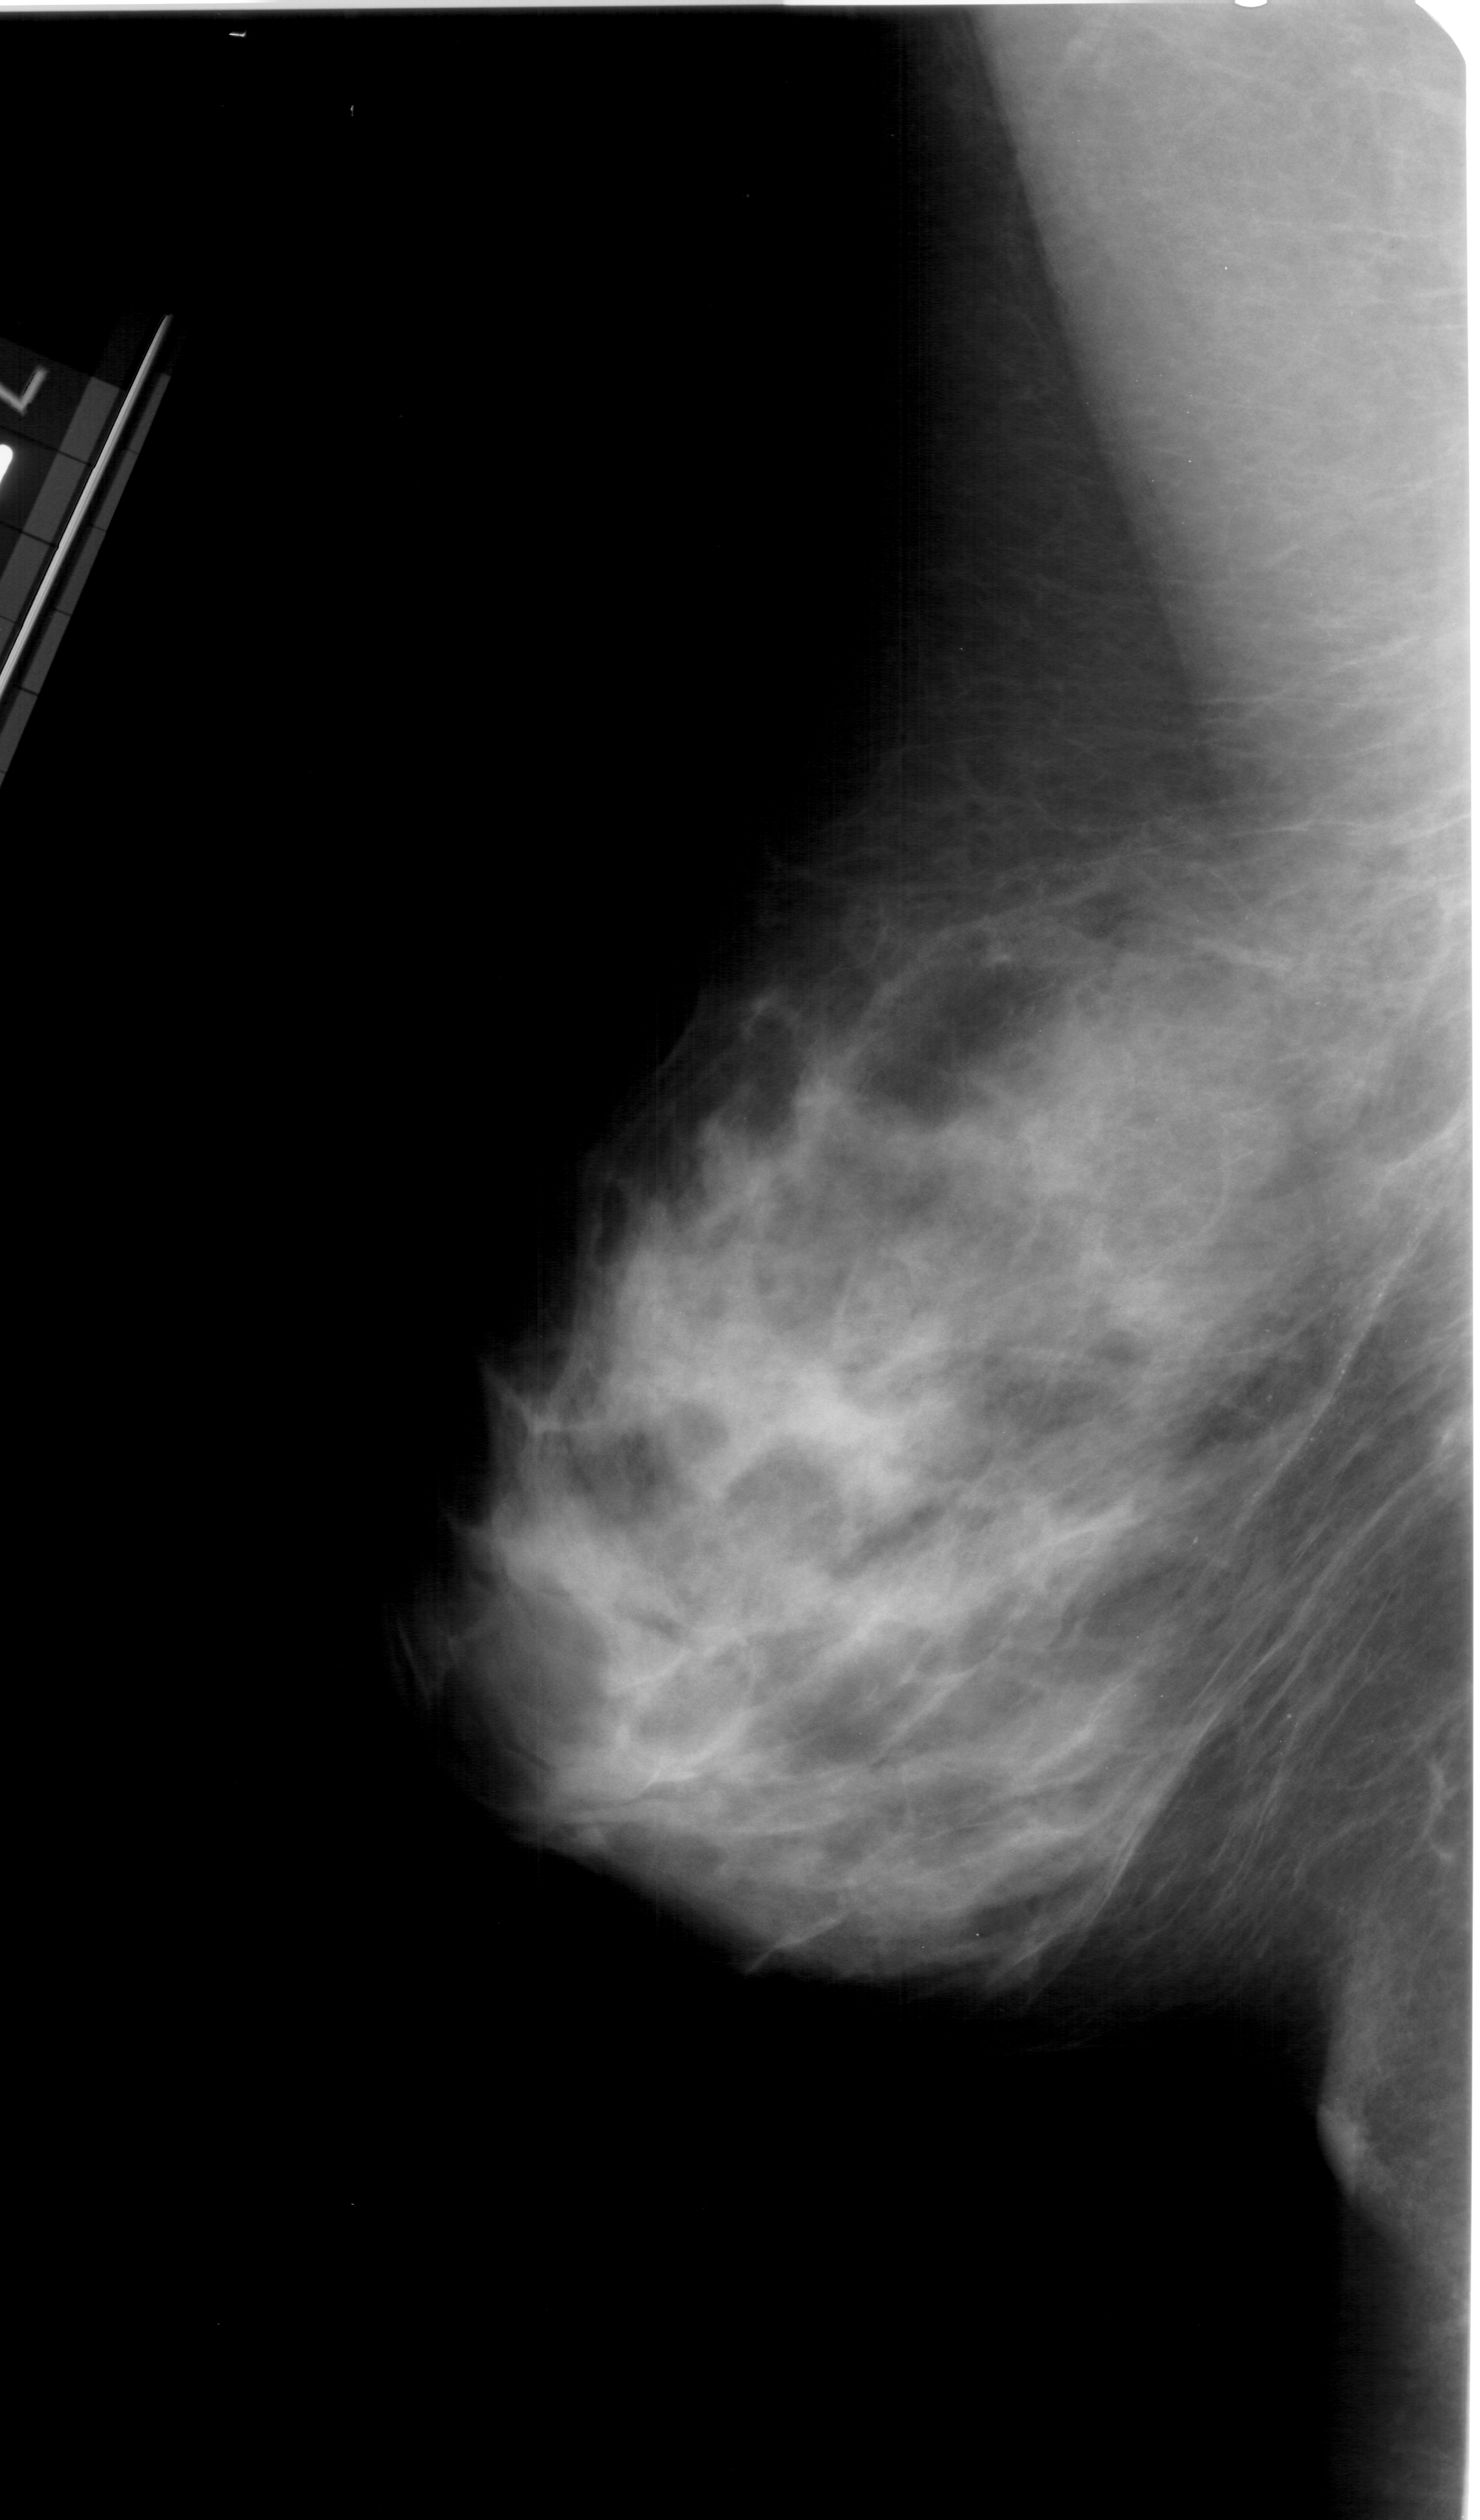
Scanned film-screen mammogram. Left breast. MLO view. Breast composition: extremely dense (BI-RADS density category 4 of 4). 1480 × 2520 image matrix.
Marked abnormalities (boxes around the expert regions of interest):
- calcifications, morphology pleomorphic, distribution segmental; BI-RADS assessment category 4; subtlety rating 4 on a 1 (subtle) to 5 (obvious) scale; pathology (as recorded): benign: bounding box <1032,1118,1453,1643> (left, top, right, bottom; pixels)